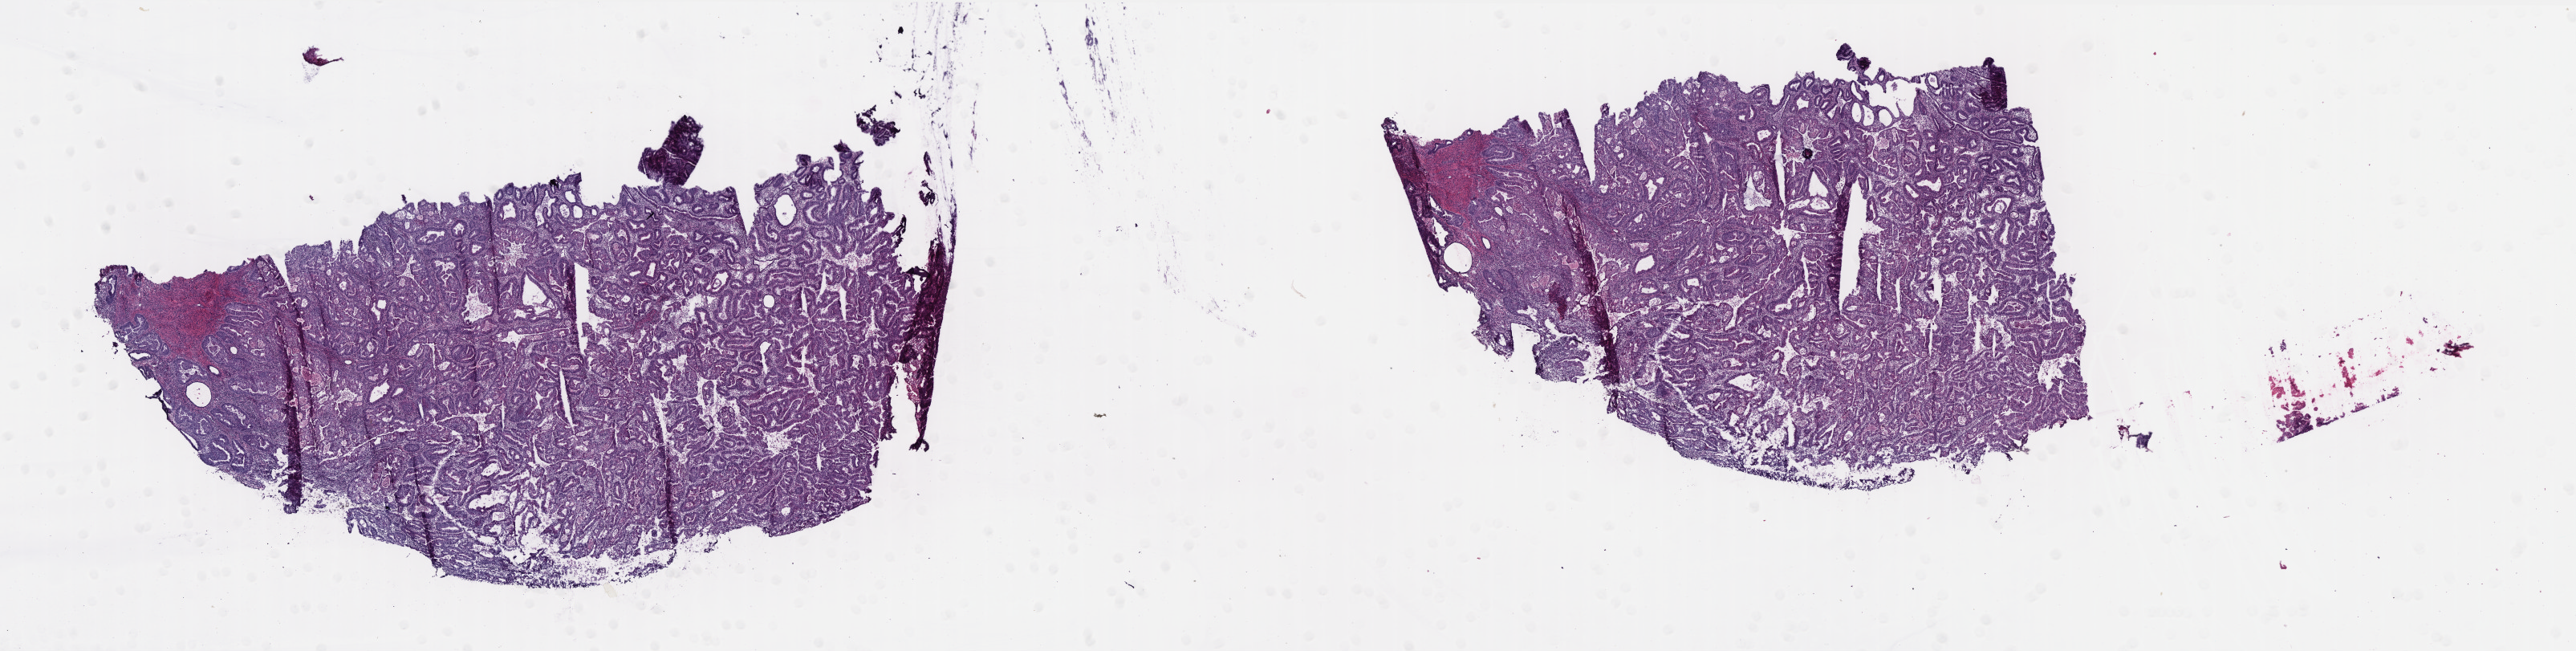
H&E whole-slide image, a low-resolution overview of the entire scanned area, about 25.7 x 6.5 mm (from a 40x scan). Frozen section. Primary tumour sample from the uterus. Female patient; age at initial diagnosis 61 years. Histologic grade: G3 (poorly differentiated). Slide review estimates, as recorded: tumour cells 75%, tumour nuclei 75%, normal cells 0%, stromal cells 25%, necrosis 0%. Infiltration values recorded for this section: lymphocyte infiltration 0%, monocyte infiltration 0%, neutrophil infiltration 0%.
FIGO stage: IIIC. Histologic diagnosis: Serous cystadenocarcinoma, NOS (endometrium).